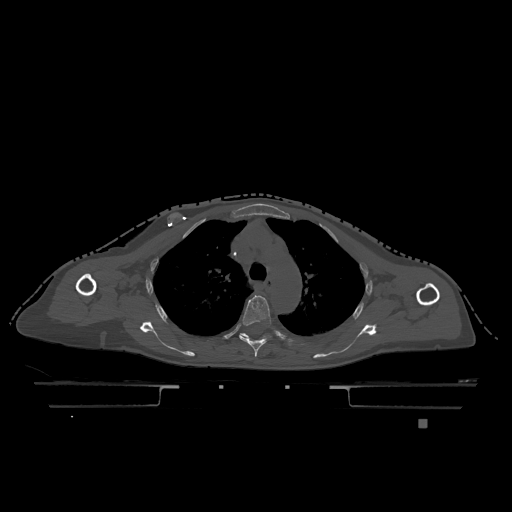
CT including the spine, one axial slice; slice 872 of 1317 in the series (ordered by position); bone window (W 1800 / L 400 HU); 0.5 mm slice thickness; 512 × 512 image matrix, field of view 500 × 500 mm. Patient: female, 74 years. Case-level facts recorded for this patient, not image findings: primary cancer: lung.
Structures marked on this image (semi-automatic segmentation, software-assisted and operator-edited):
- T4 vertebra: bounding box (x1, y1, x2, y2) in pixels: (239, 296, 271, 357)
- T5 vertebra: (240, 333, 265, 338)